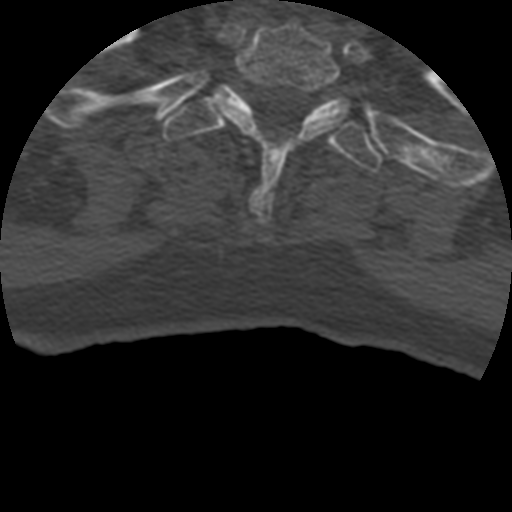
CT including the spine, one axial slice. Slice 376 of 399 in the series (ordered by position). 120 kVp. Bone window (W 1800 / L 400 HU). 512 × 512 image matrix, field of view 160 × 160 mm. Patient age 69 years. Case-level facts recorded for this patient, not image findings: primary cancer: prostate.
Structures marked on this image (semi-automatically segmented with operator editing):
- T1 vertebra: bounding box <220,24,354,218> (left, top, right, bottom; pixels)
- T2 vertebra: <164,84,382,172>